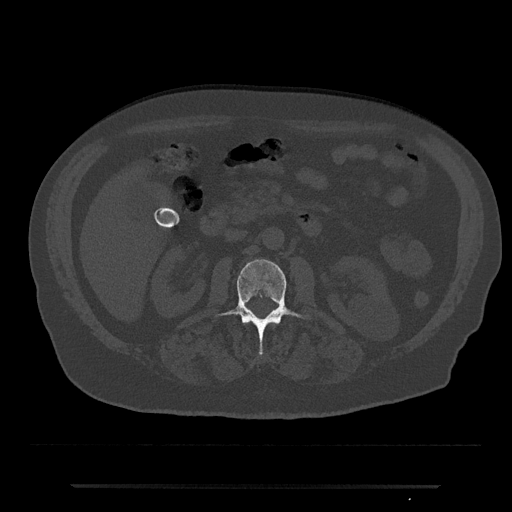
CT including the spine, one axial slice; slice 472 of 797 in the series (ordered by position); 120 kVp; bone window (W 1800 / L 400 HU); 0.5 mm slice thickness; 512 × 512 image matrix, field of view 434 × 434 mm. Male patient, age 80 years. Case-level facts recorded for this patient, not image findings: primary cancer: prostate; vertebrae with lytic lesions (as recorded): L1, T11.
Outlined on this slice (semi-automatic segmentation, software-assisted and operator-edited):
- L2 vertebra: bounding box <215,259,311,356> (left, top, right, bottom; pixels)